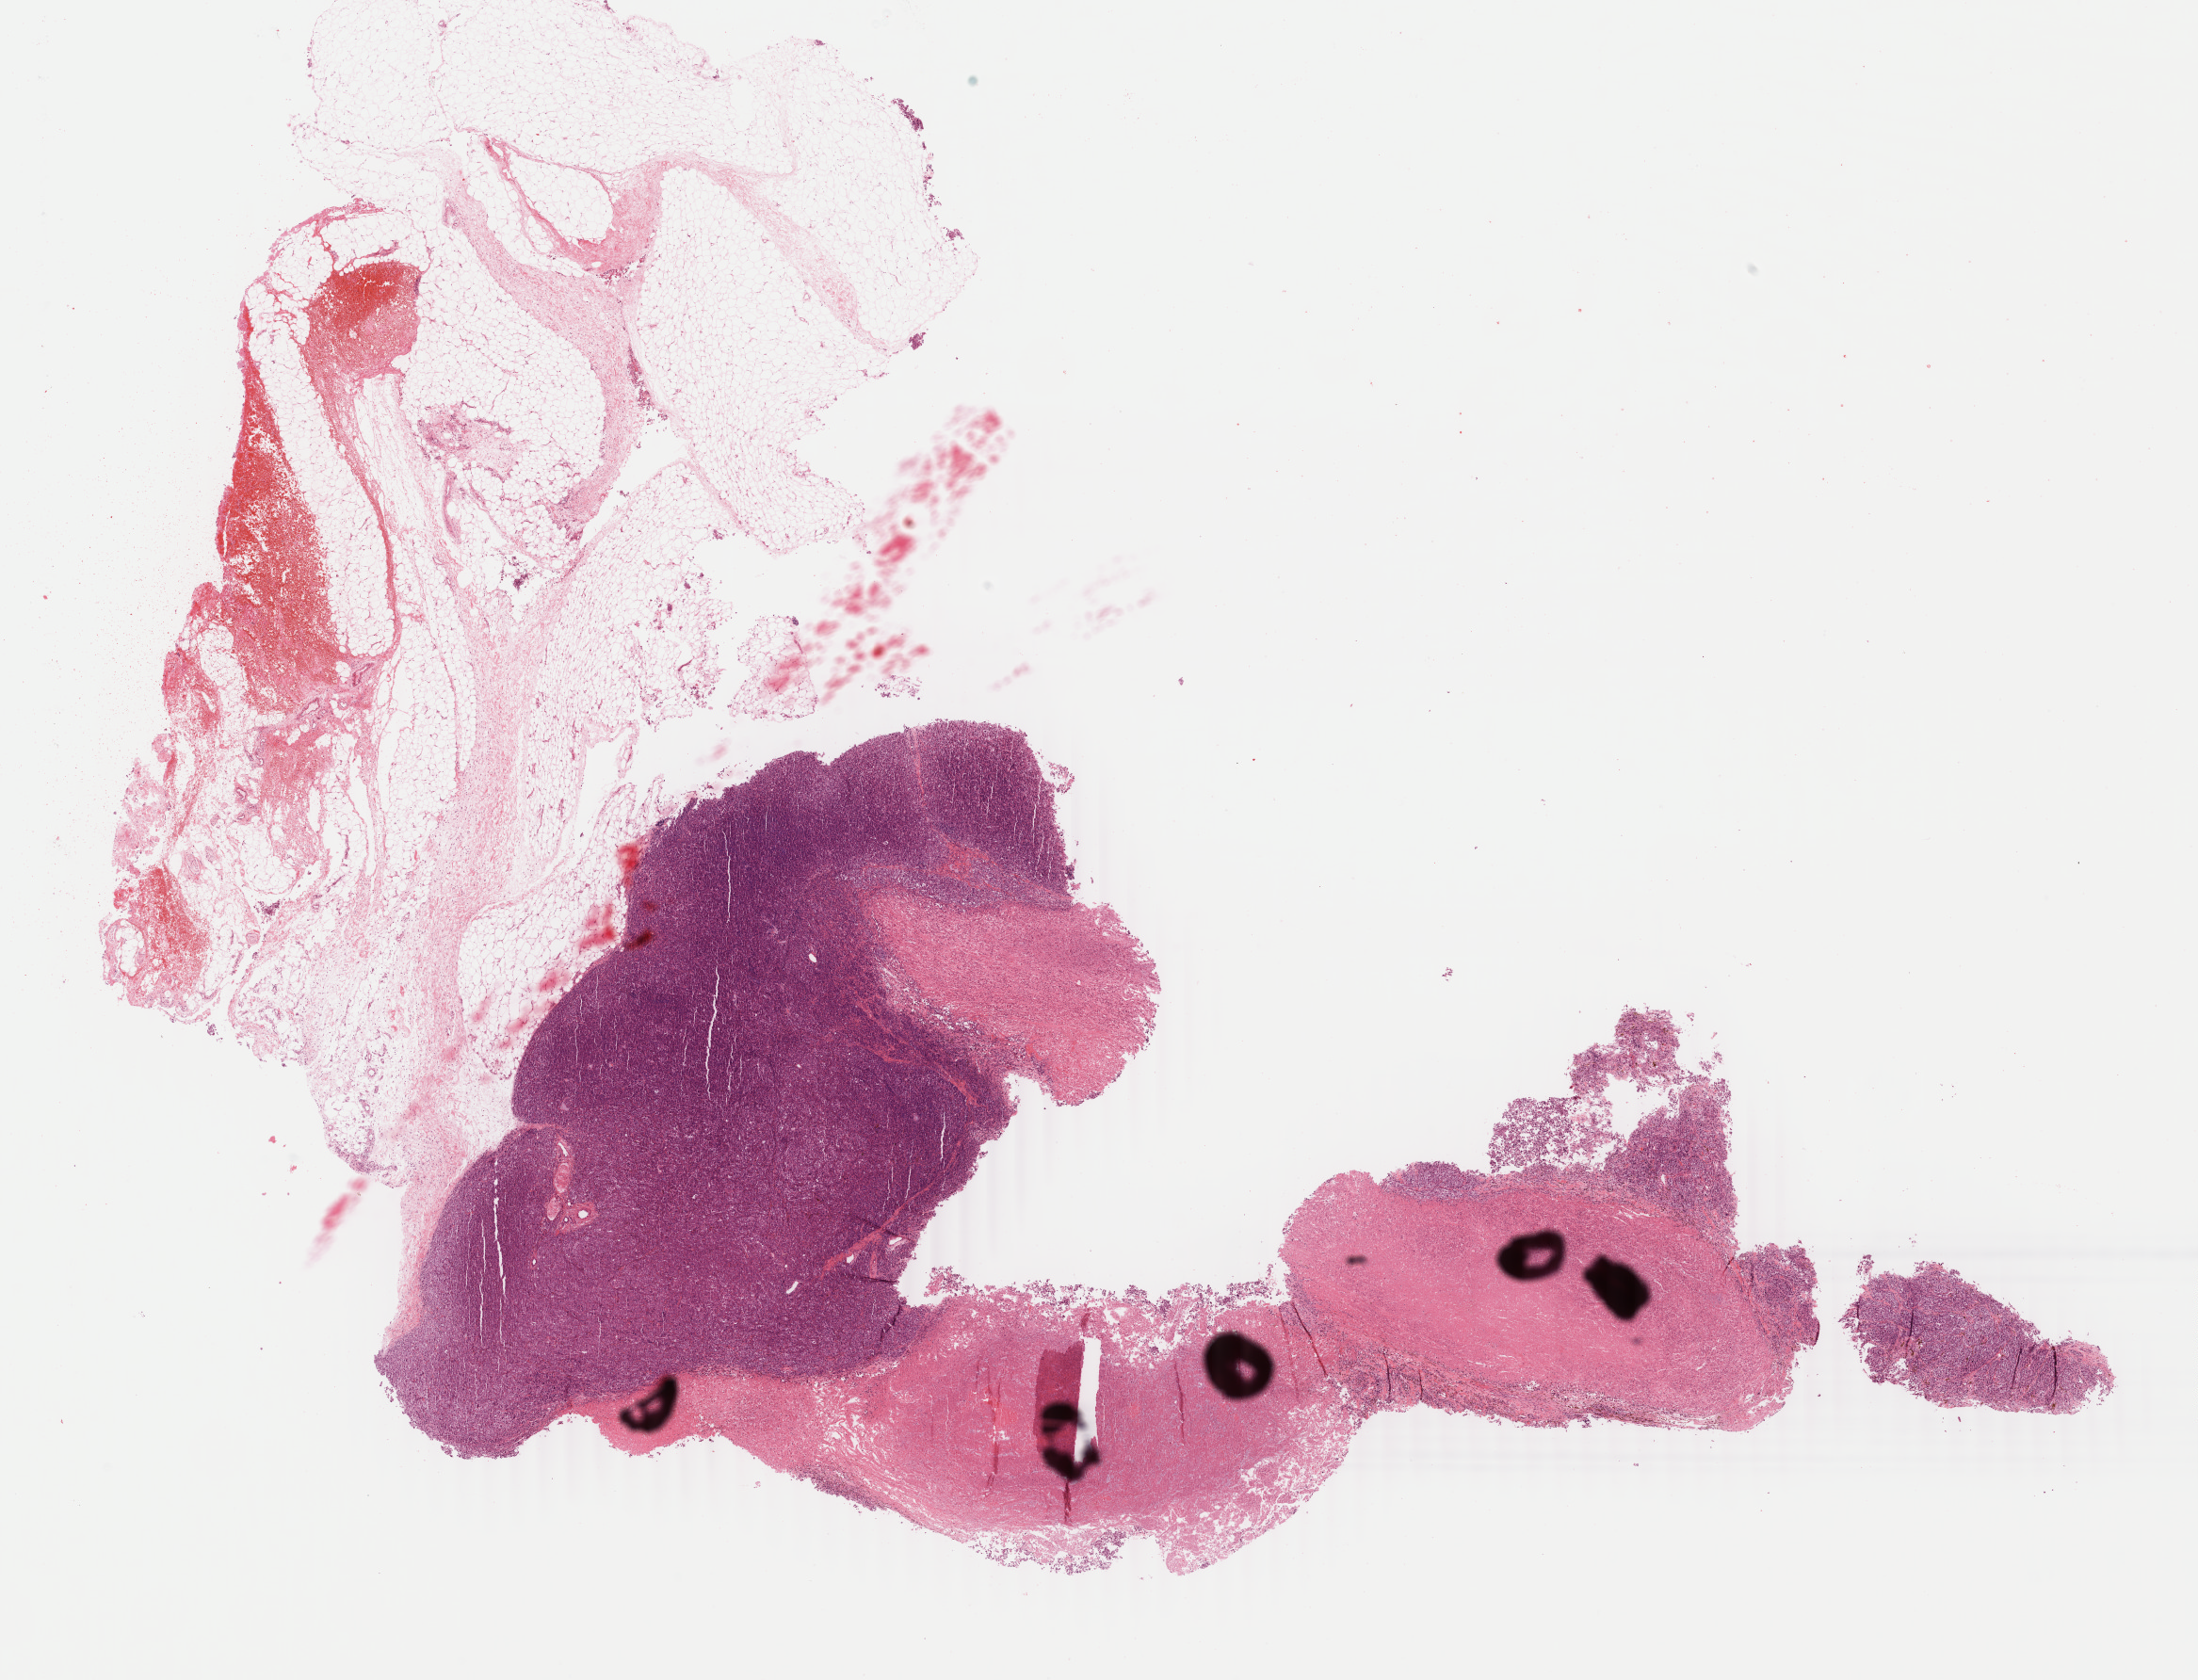
H&E-stained whole-slide image — whole scanned area (about 18.6 x 14.2 mm) shown as a low-resolution overview. Formalin-fixed paraffin-embedded (FFPE) diagnostic section. Skin, primary tumour sample. Patient: female, age at initial diagnosis 76 years.
• AJCC pathologic stage: IIC (7th edition)
• TNM: T4b N0 M0
• diagnosis: Nodular melanoma